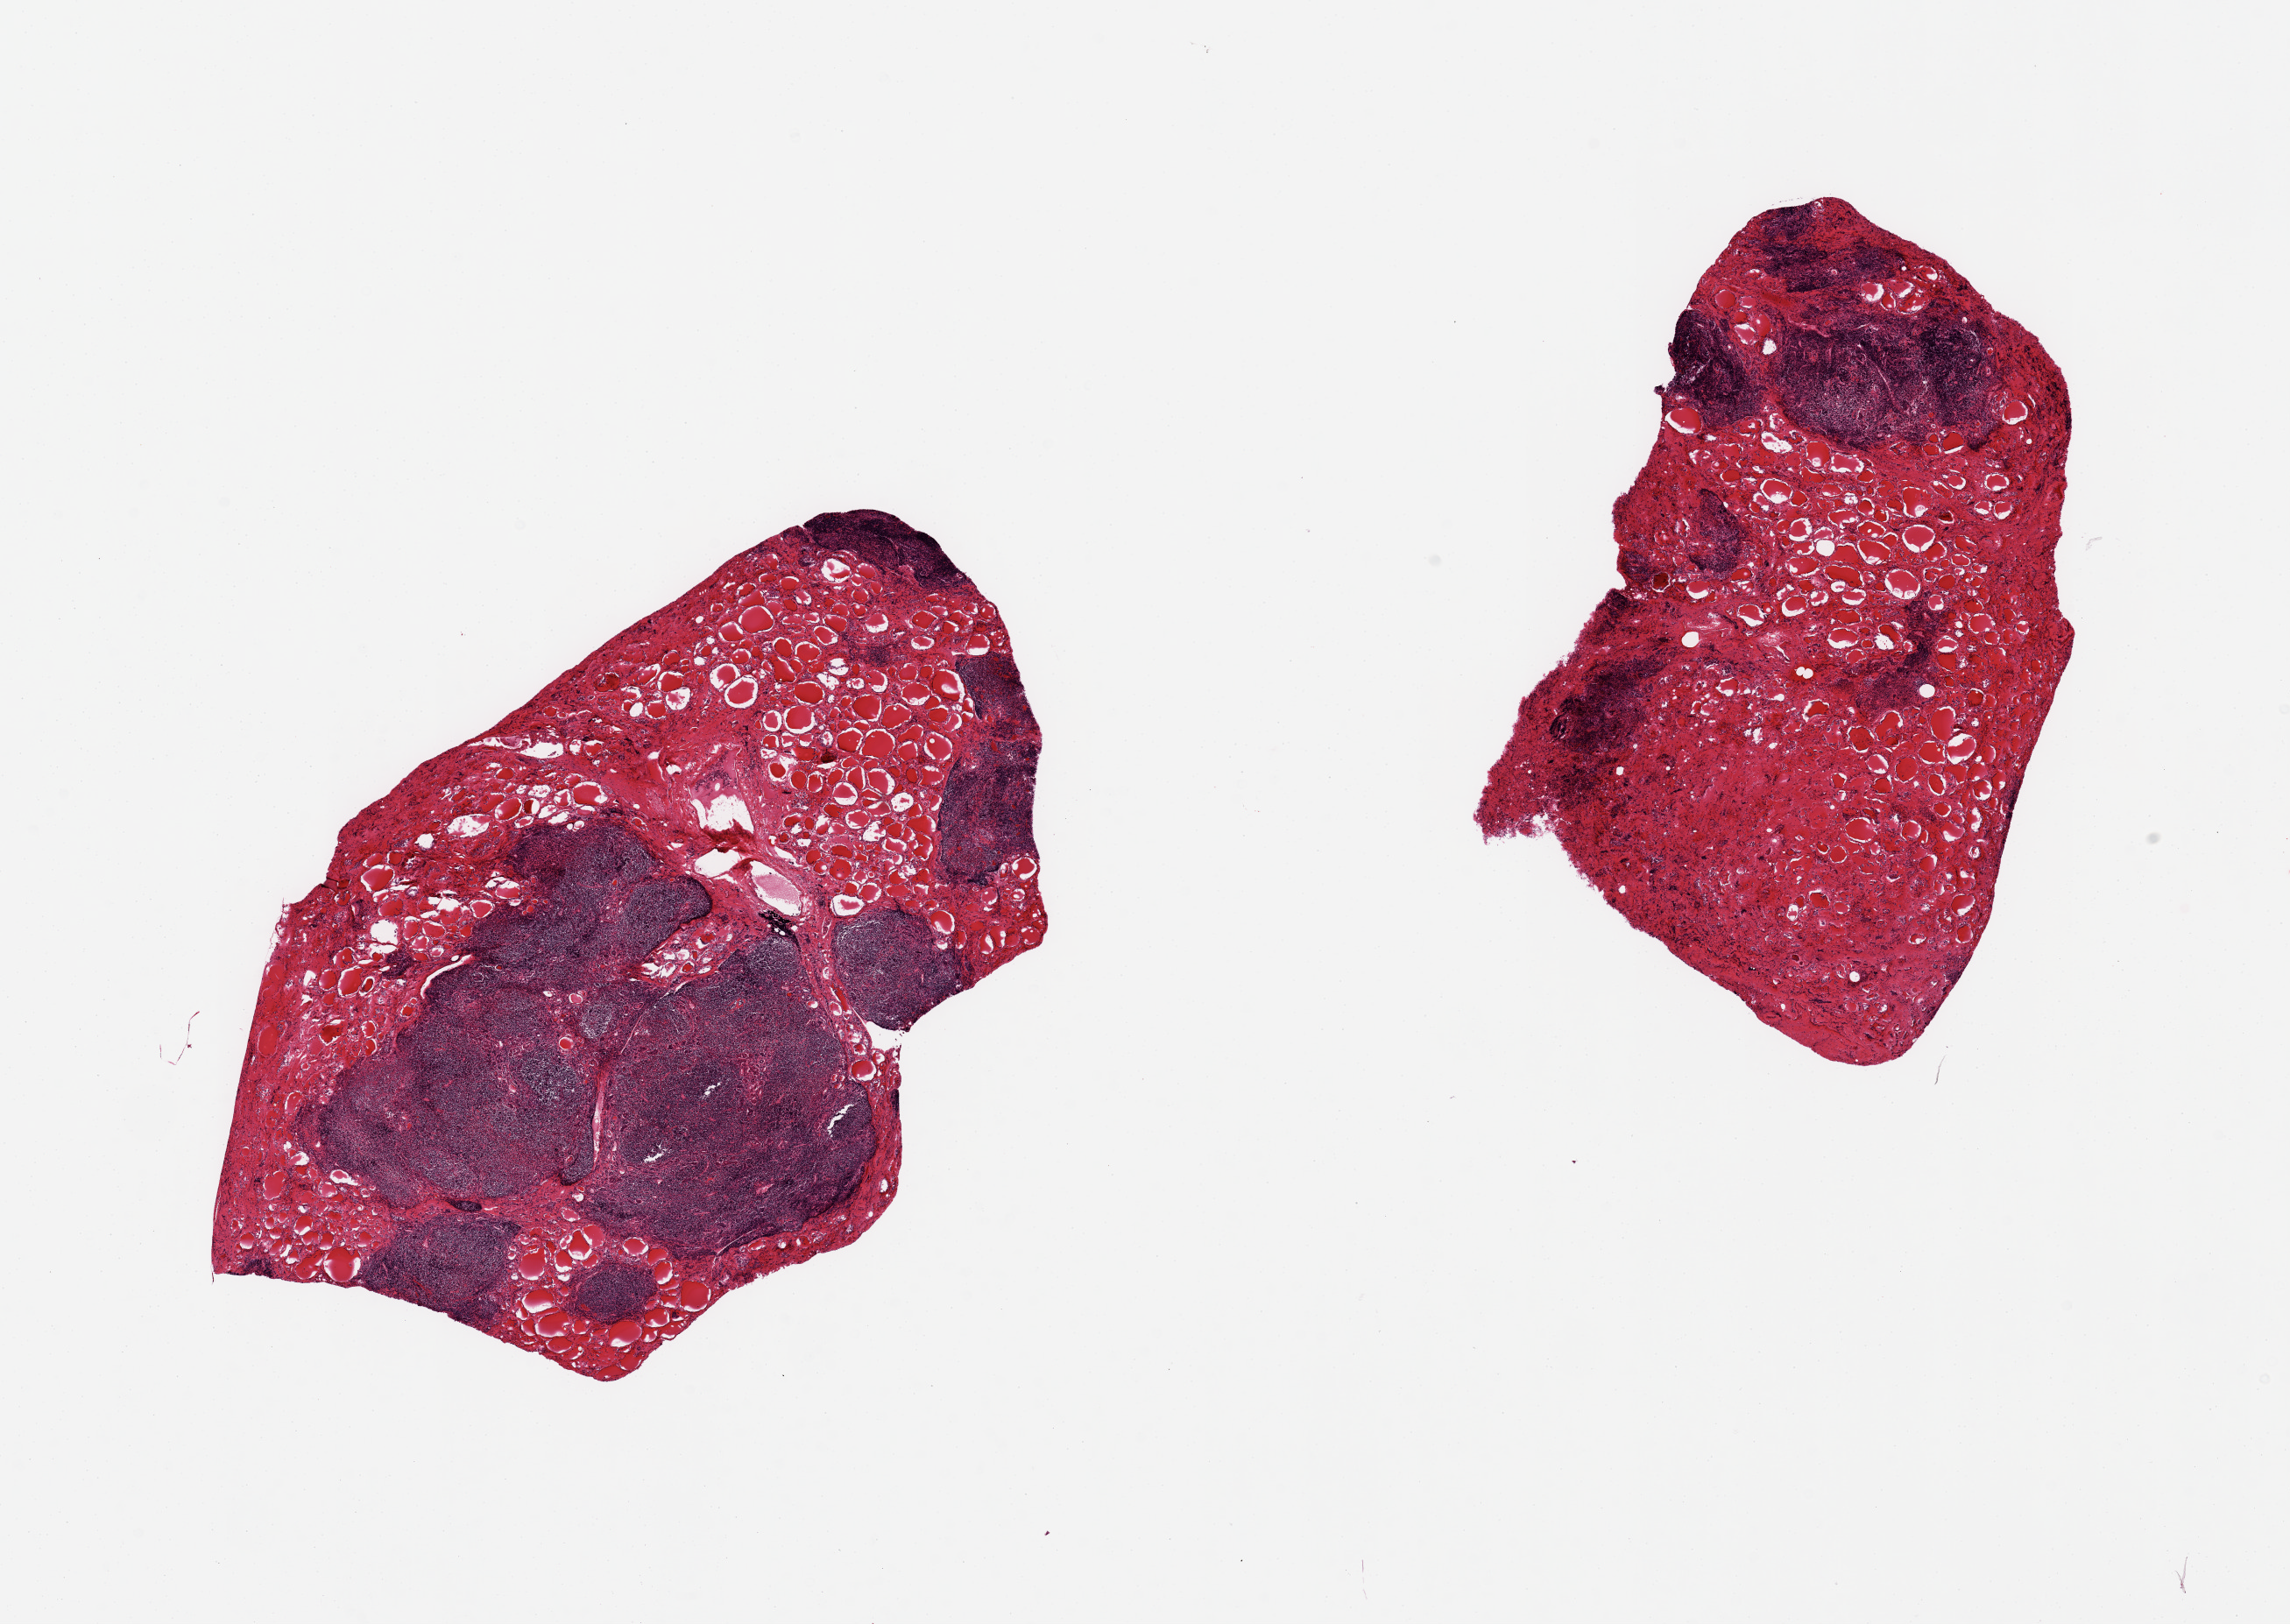
Whole-slide image, haematoxylin and eosin stain, a low-resolution overview of the entire scanned area, about 20.7 x 14.7 mm, PAXgene-fixed, paraffin-embedded tissue, section of thyroid (target tissue), donor tissue sample. Male donor.
- reviewer comment on this tissue sample: 2 pieces, Hashimoto's thyroiditis with atypical lymphoid infiltrate